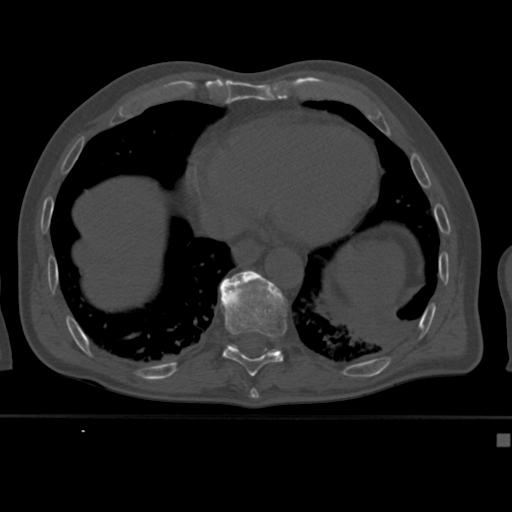
CT including the spine, one axial slice; slice 226 of 430 in the series (ordered by position); bone window (W 1800 / L 400 HU); 1.5 mm slice thickness; 512 × 512 image matrix. Patient: male, 64 years. Case-level facts recorded for this patient, not image findings: primary cancer: uterus; vertebrae with lytic lesions (as recorded): T1, T4, T5, T7, L5.
Structures marked on this image (semi-automatic segmentation, software-assisted and operator-edited):
- T10 vertebra: bounding box <219,271,287,377> (left, top, right, bottom; pixels)
- T11 vertebra: <222,270,252,347>